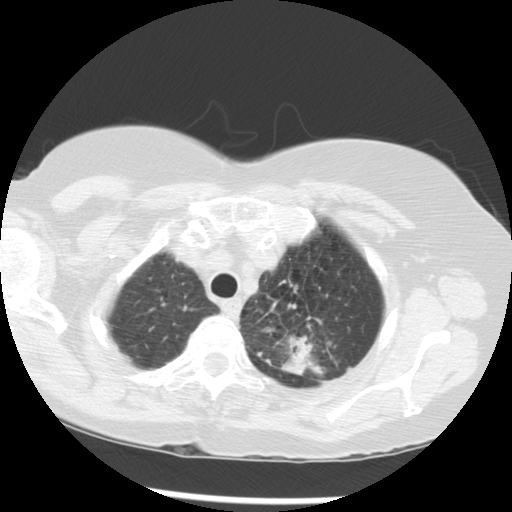
Low-dose screening chest CT, axial slice. Third annual screen. Lung window (W 1500 / L -600 HU). Standard (soft-tissue) reconstruction kernel (STANDARD). 120 kVp. 512 × 512 image matrix. Female participant, aged 70 years at enrolment. Current smoker at enrolment.
Expert reader's lesion annotation, bounding box [x1, y1, x2, y2] px = [248, 290, 347, 378]. Reader record for this screening exam (exam-level; its link to the box is not recorded): non-calcified nodule or mass ≥4 mm, left upper lobe, 32 × 26 mm, spiculated (stellate) margins, soft tissue attenuation, pre-existing on the prior screen: yes; interval growth: yes. Official screen result: positive, other.